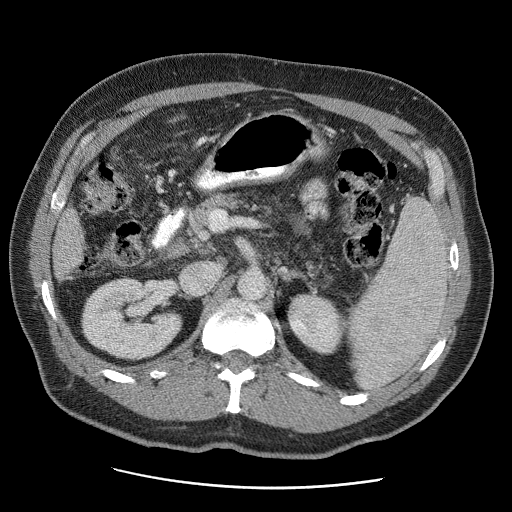
Contrast-enhanced abdominal CT (liver protocol), one axial slice. Position 12 of 81 along the scan axis. Reconstruction kernel STANDARD. 120 kVp. Soft-tissue window (W 400 / L 40 HU). 512 × 512 image matrix. Case-level facts recorded for this patient, not image findings: diagnosis: hepatocellular carcinoma (patient treated with transarterial chemoembolisation; whether this scan precedes or follows treatment is not stated here); TNM stage (as recorded): Stage-IIIA; Child-Pugh class: A; tumour nodularity: multinodular.
Annotated regions visible in this slice (semi-automatically segmented with operator editing):
- liver parenchyma outside the tumour (the mass and vessels are separate outlines, so this box may not span the whole liver): bounding box (x1, y1, x2, y2) in pixels: (54, 208, 84, 280)